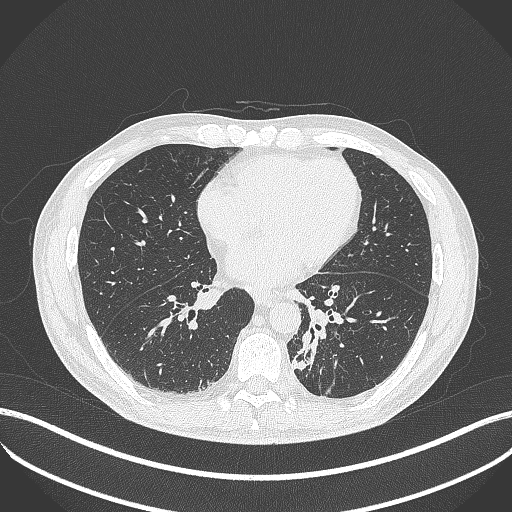
Chest CT, one axial slice. Position 162 of 451 along the scan axis. 120 kVp. Lung window (W 1500 / L -600 HU). 1 mm slice thickness. 512 × 512 image matrix. Patient: male, 72 years. From the clinical record (not read from this slice): clinical TNM (as recorded): T2b N0 M1.
Annotated regions visible in this slice (bounding box drawn by a radiologist):
- lung tumour (recorded histology: adenocarcinoma): bounding box [x1, y1, x2, y2] px = [292, 323, 321, 374]